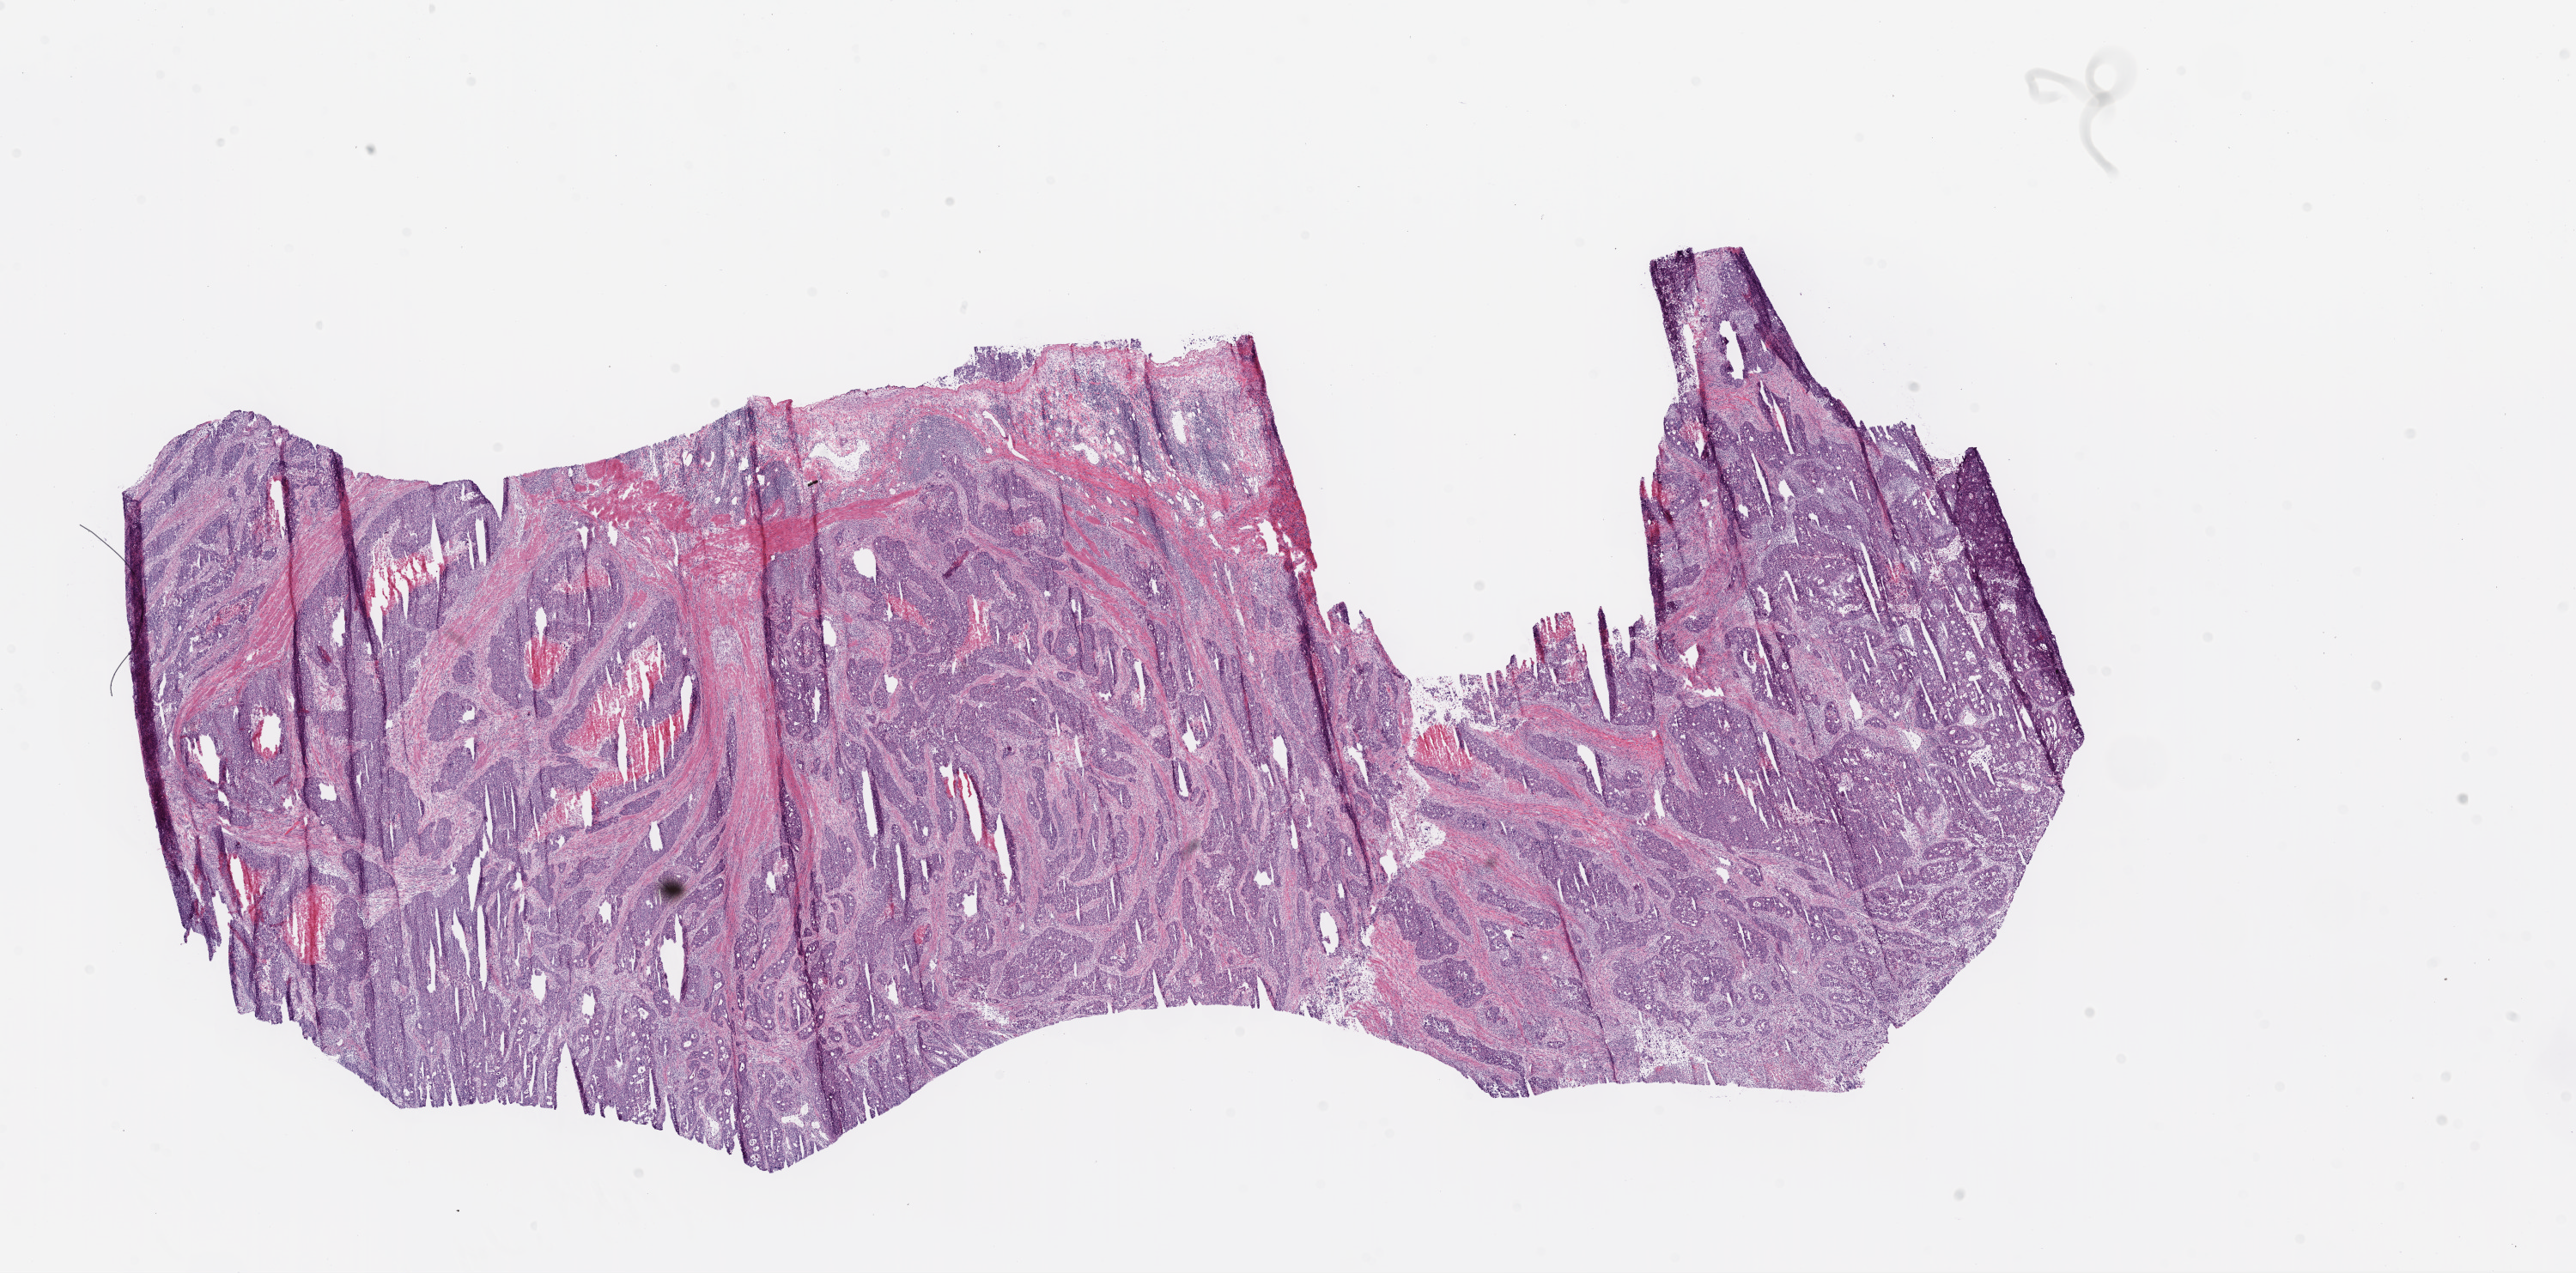
Whole-slide histology image, H&E, low-resolution overview of the scanned area, about 24.1 x 11.9 mm, frozen section from the bottom of the tissue portion, primary tumour sample from the colon. Patient: female, age at initial diagnosis 81 years. Slide review estimates, as recorded: tumour cells 82%, tumour nuclei 70%, normal cells 0%, stromal cells 10%, necrosis 8%.
Lymph nodes positive (case pathology): 0 of 33 examined. AJCC pathologic stage: IIA (6th edition). Diagnosis: Adenocarcinoma, NOS.